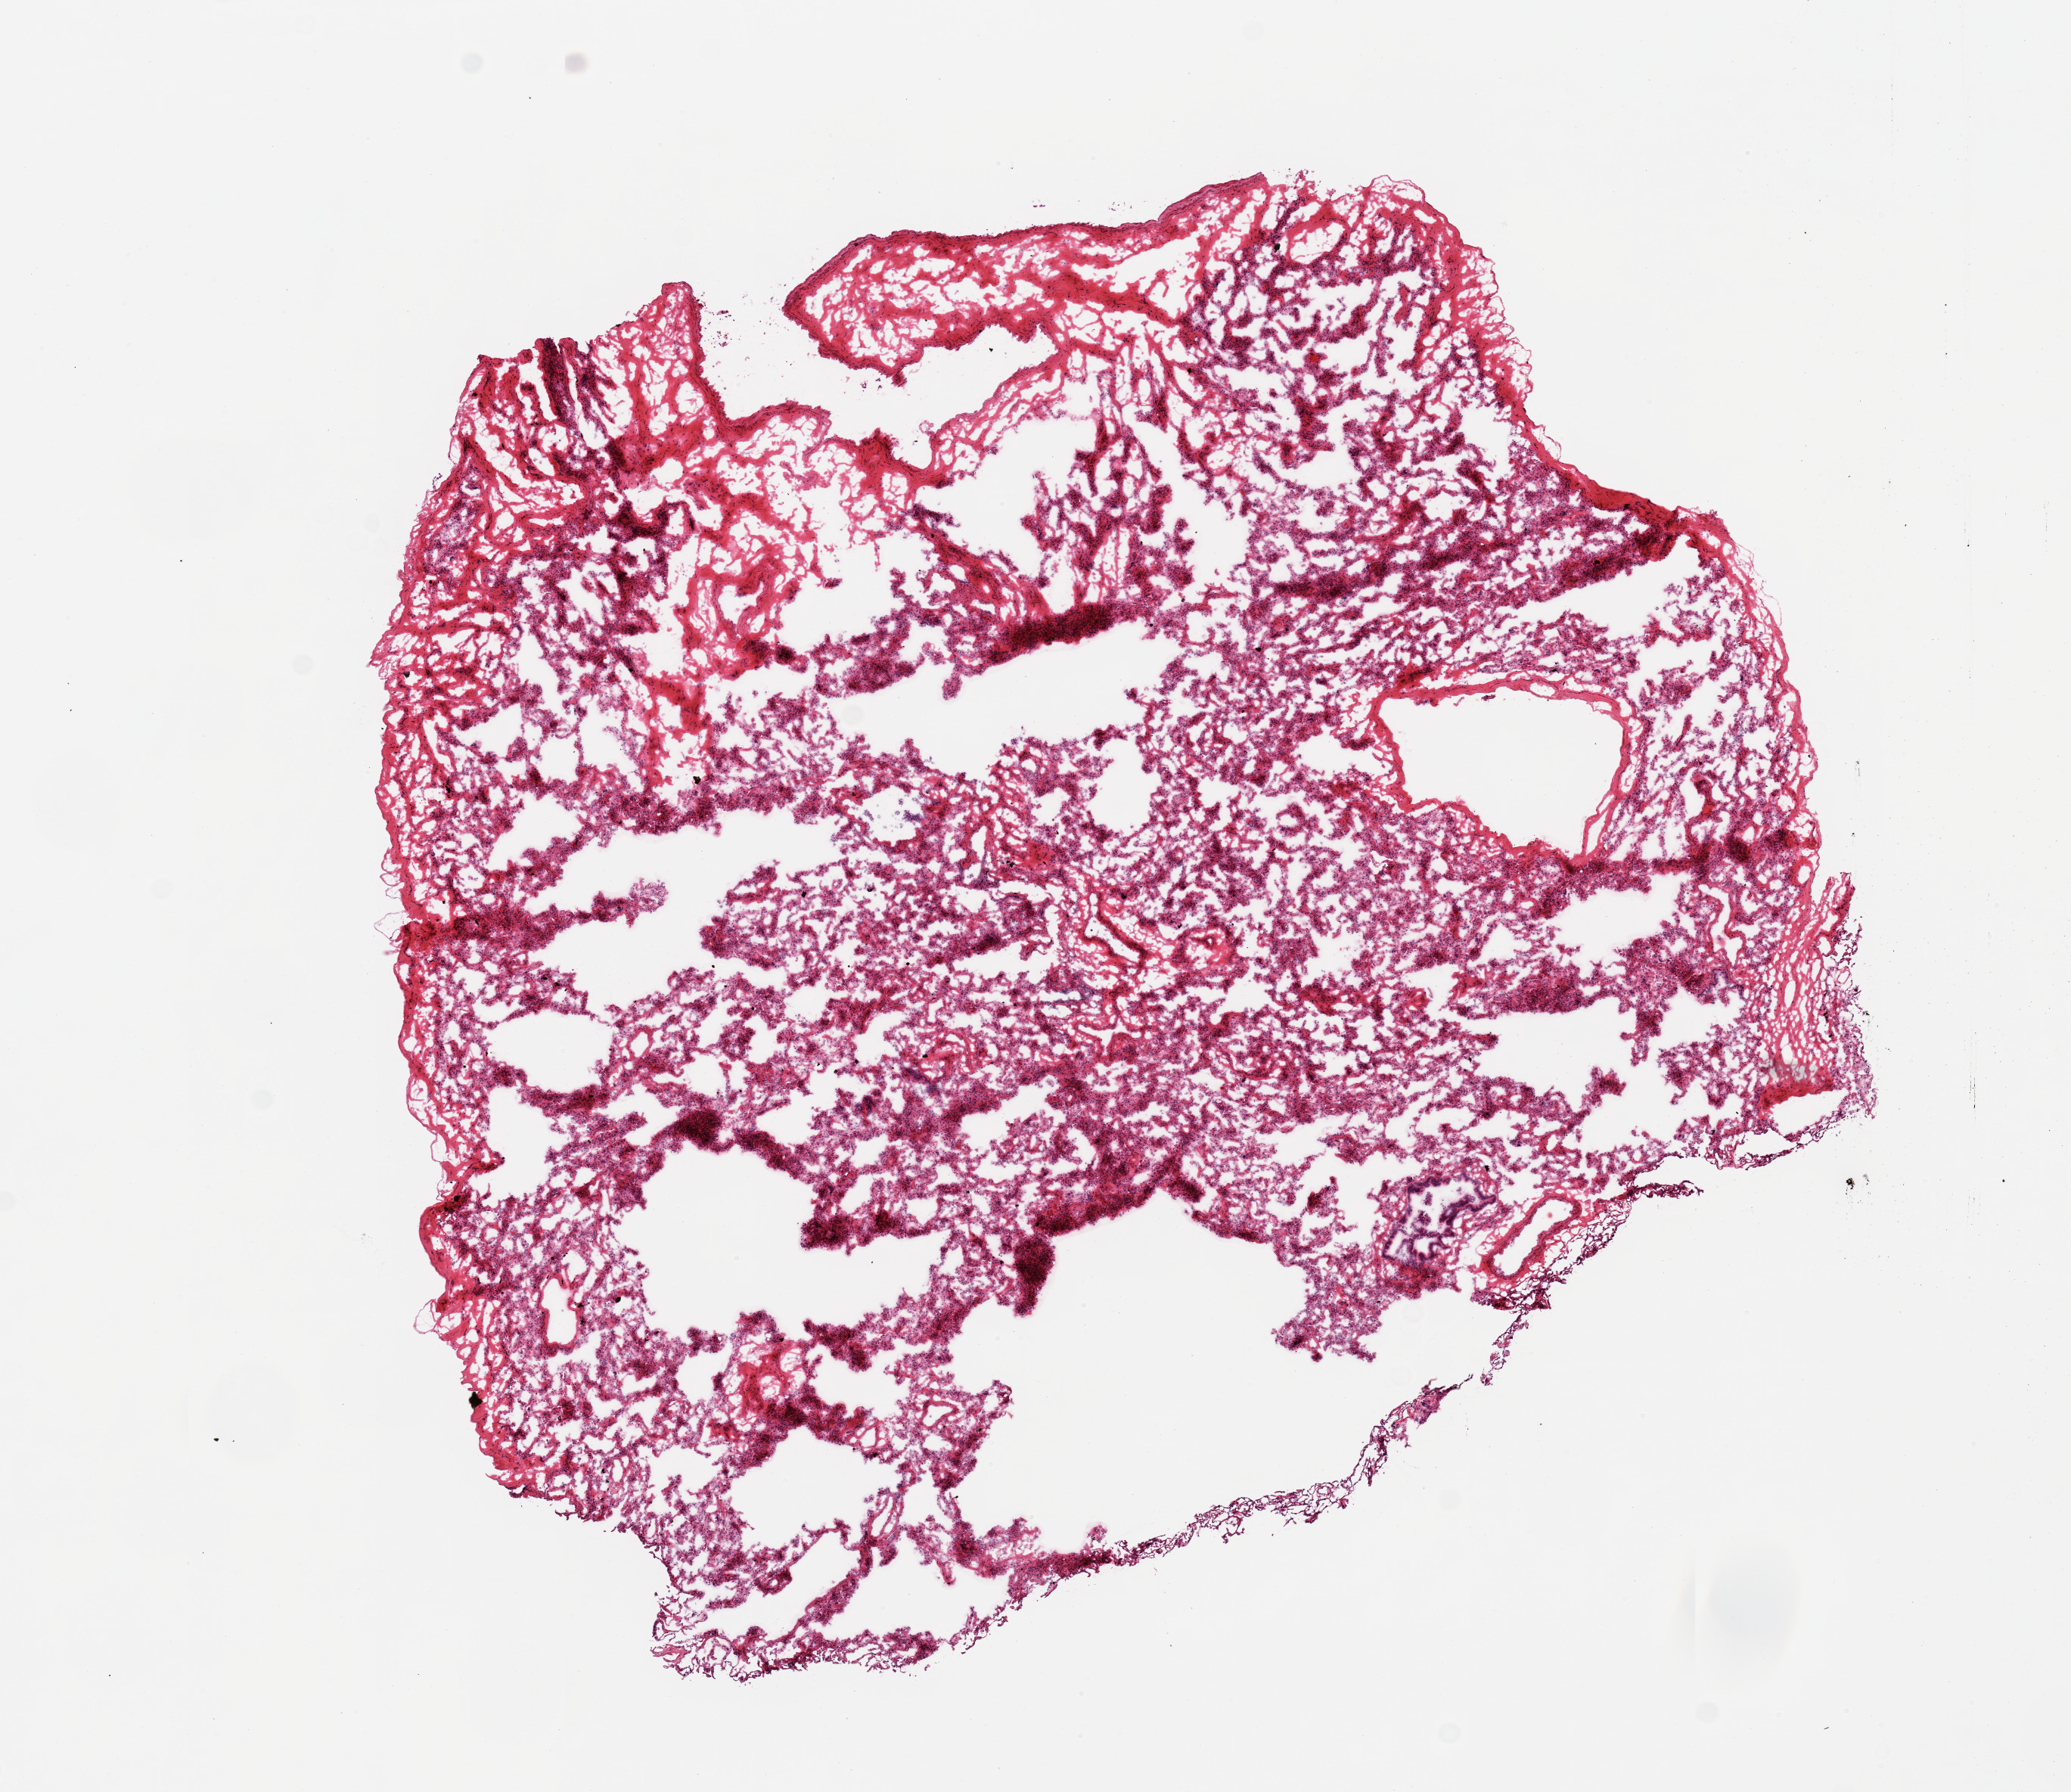
Whole-slide image, hematoxylin and eosin (H&E) stain, brightfield, a low-resolution overview of the entire scanned area, about 10.8 x 9.4 mm (acquisition: 20x scan). Frozen section. Sampled site (target tissue): lung. Tissue donor sample. Donor: female.
- pathologist's review note for this sample: 1 piece